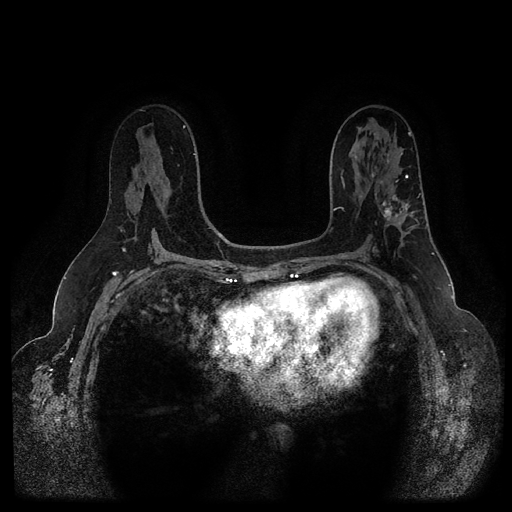
Breast MRI (dynamic contrast-enhanced, multi-phase), one axial slice. Slice 58 of 116 in the series (ordered by position). Dynamic contrast-enhanced series, time point 2 of 5 at this slice position (early post-contrast). 1.5 T. TE 2.6 ms, TR 5.3 ms. 2 mm slice thickness. 512 × 512 image matrix, field of view 350 × 350 mm. Patient: female, 54 years.
Structures marked on this image (semi-automatically segmented with operator editing):
- breast lesion (labelled 'tumour' in the annotation; benign lesions carry a separate 'benign' label): bounding box <379,194,408,225> (left, top, right, bottom; pixels)